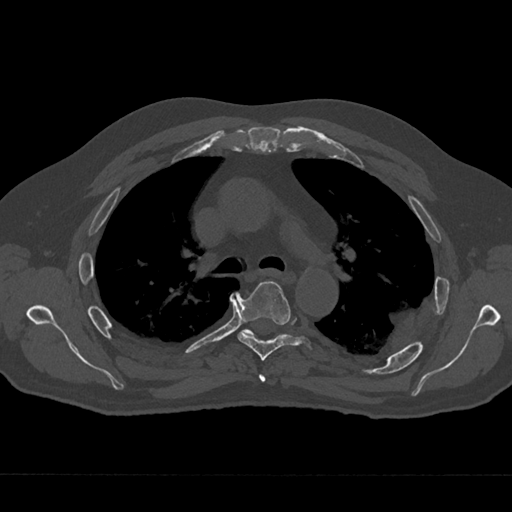
CT including the spine, one axial slice. Position 468 of 797 along the scan axis. Reconstruction kernel Br40s/3. Bone window (W 1800 / L 400 HU). 512 × 512 image matrix. Patient: male, 75 years. From the clinical record (not read from this slice): primary cancer: renal; vertebrae with lytic lesions (as recorded): T4.
Outlined on this slice (semi-automatically segmented with operator editing):
- T4 vertebra: box from (x=259, y=374) to (x=266, y=382) px
- T5 vertebra: (x=236, y=281)–(x=313, y=361)
- T6 vertebra: (x=241, y=329)–(x=254, y=336)